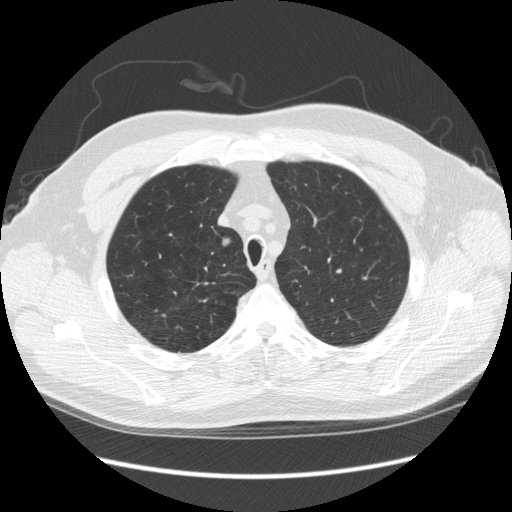
Low-dose screening chest CT, axial slice, third annual screen, lung window (W 1500 / L -600 HU), standard (soft-tissue) reconstruction kernel (STANDARD), 120 kVp. Male participant, aged 64 years at enrolment.
- Expert-annotated lung lesion, bounding box <196,229,241,263> (left, top, right, bottom; pixels).
- The screening reader recorded 4 non-calcified nodules or masses ≥4 mm on this exam; which of them this box marks is not recorded.
- Official screen result: positive, other.